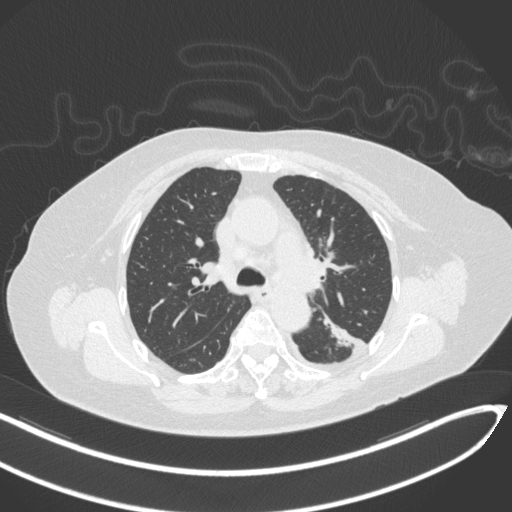
Chest CT, one axial slice; position 211 of 270 along the scan axis; reconstruction kernel B31f; lung window (W 1500 / L -600 HU); 1 mm slice thickness; 512 × 512 image matrix, field of view 400 × 400 mm. Female patient, age 76 years. From the clinical record (not read from this slice): clinical TNM (as recorded): T1c N0 M0.
Outlined on this slice (rectangle marked by the reading radiologist):
- lung tumour (recorded histology: adenocarcinoma): bounding box (x1, y1, x2, y2) in pixels: (323, 313, 362, 353)